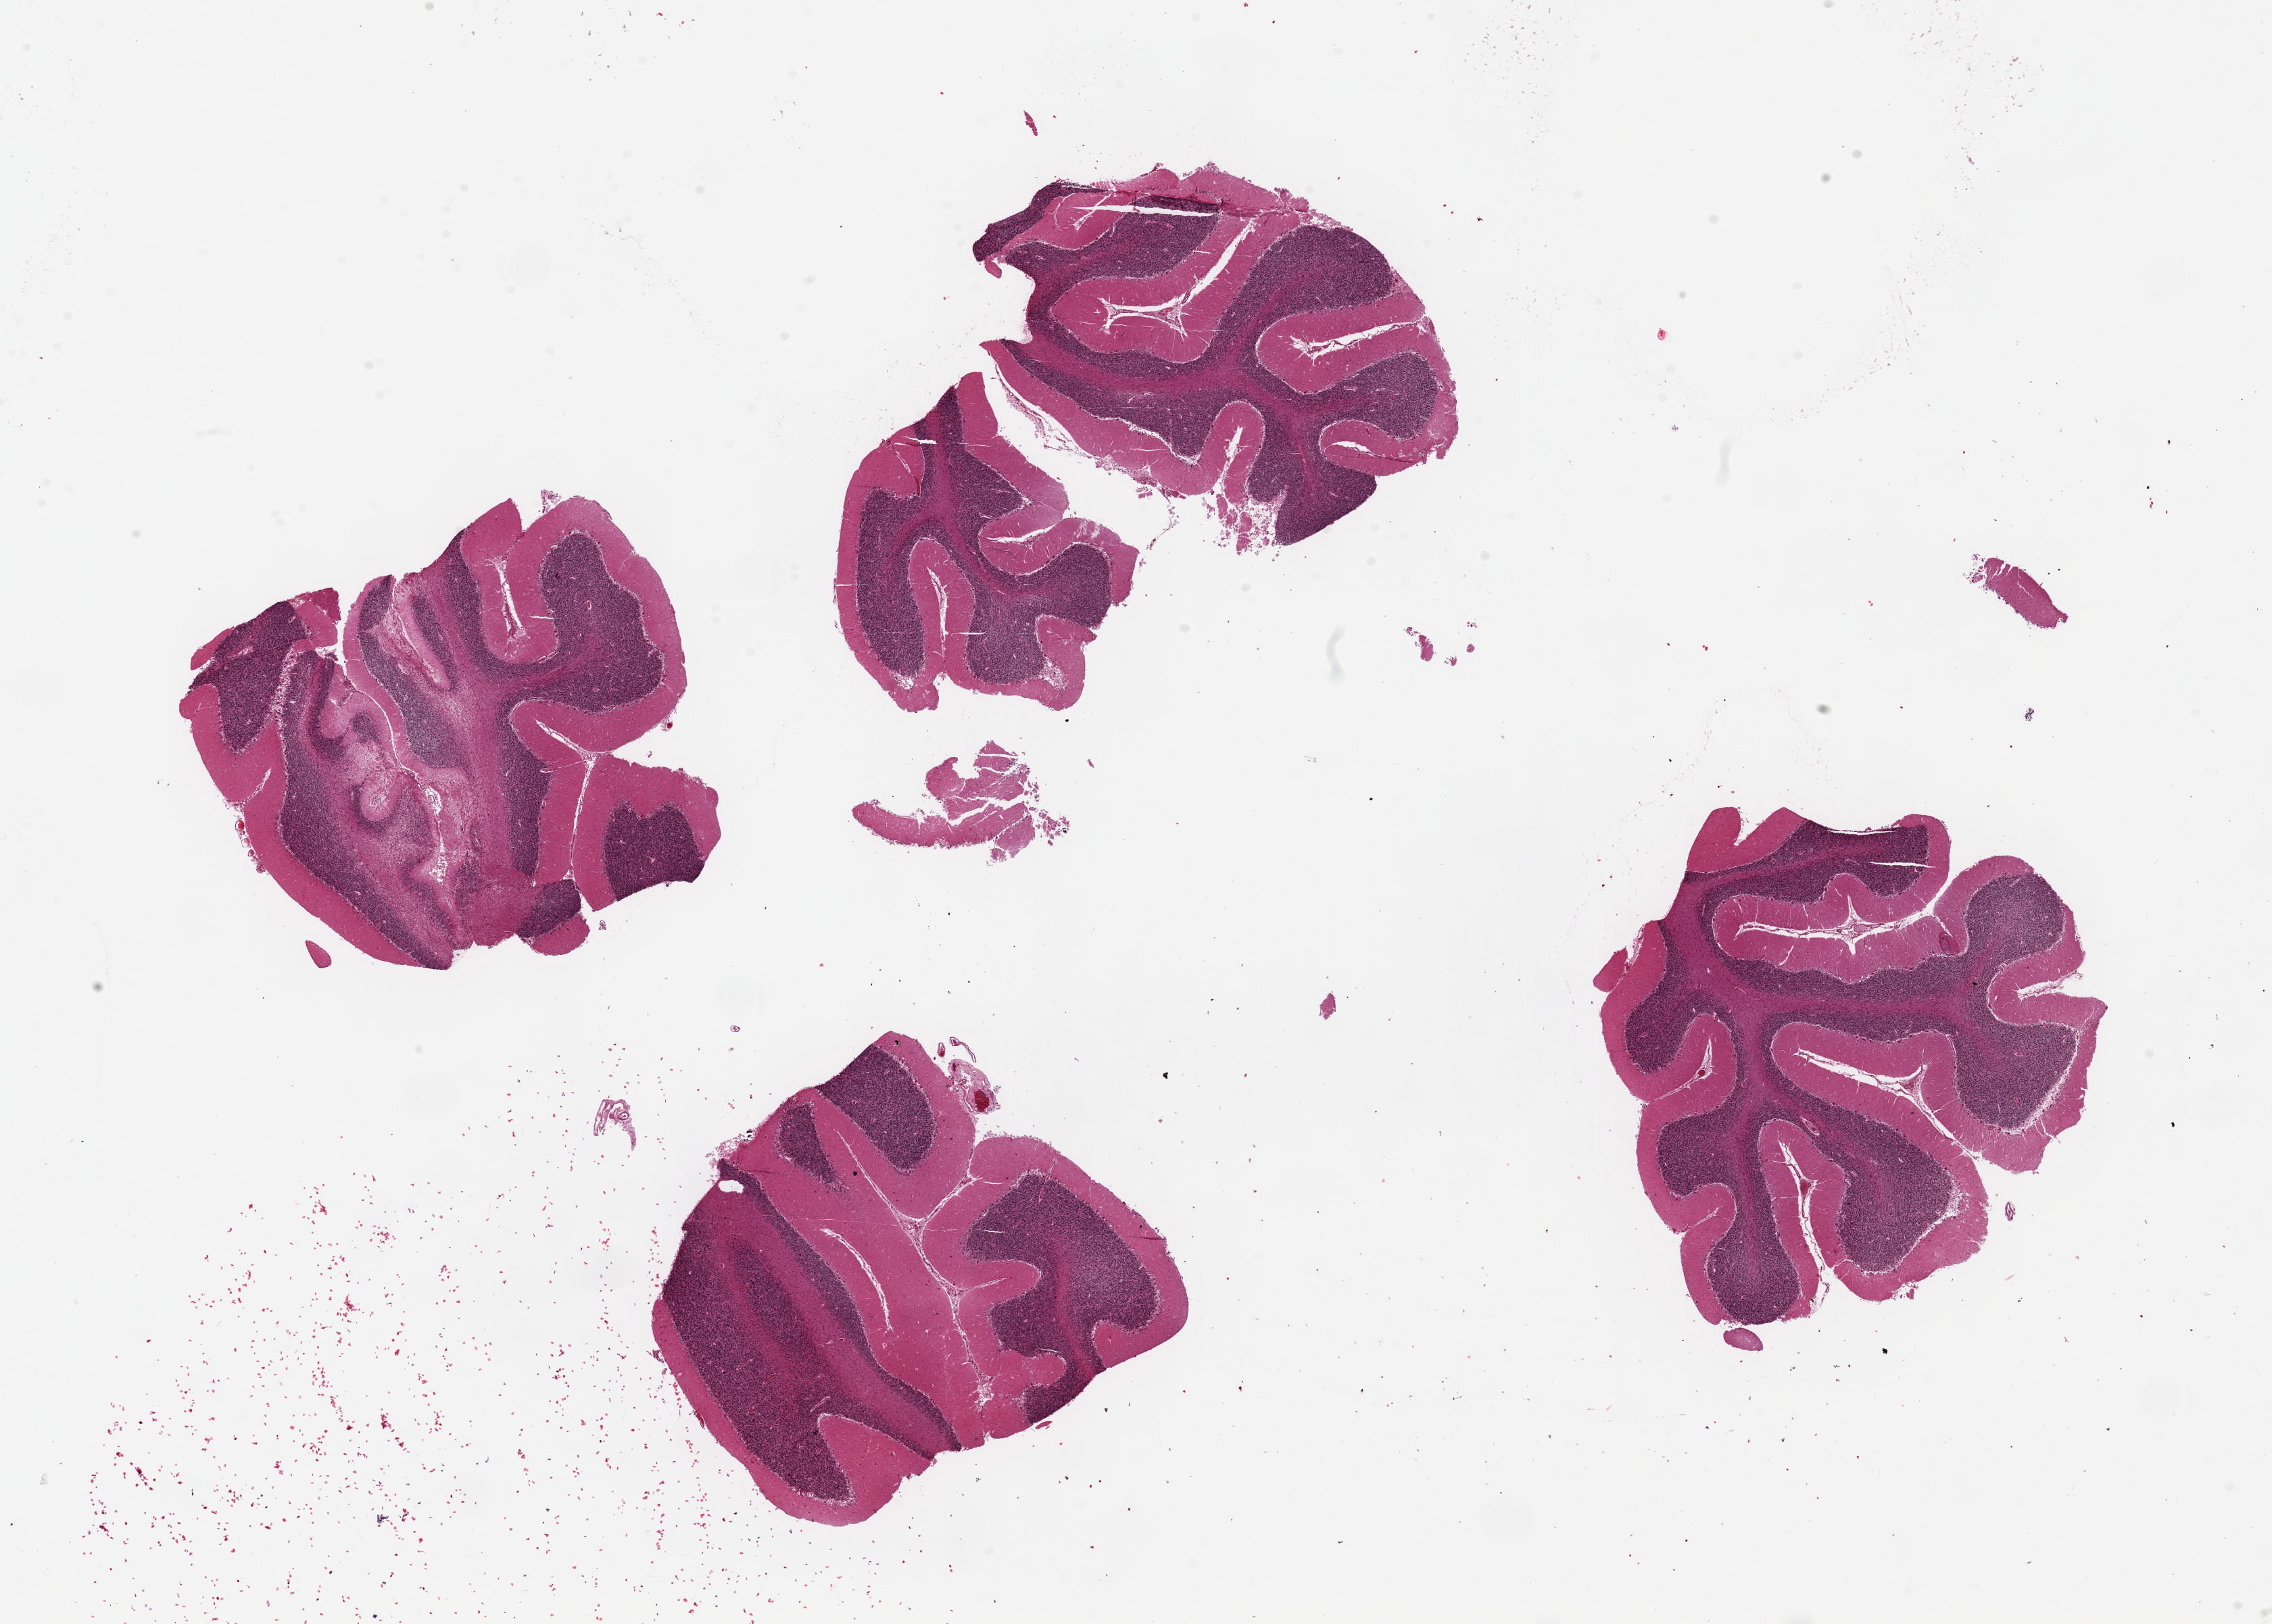
Digitized hematoxylin and eosin (H&E)-stained section, brightfield, low-resolution overview of the scanned area, about 26.6 x 19.0 mm, PAXgene-fixed, paraffin-embedded tissue, sampled site (target tissue): cerebellum, donor tissue sample. Female donor.
* review note (as recorded): 4 ~6x5mm pieces, granular layer more autolyzed